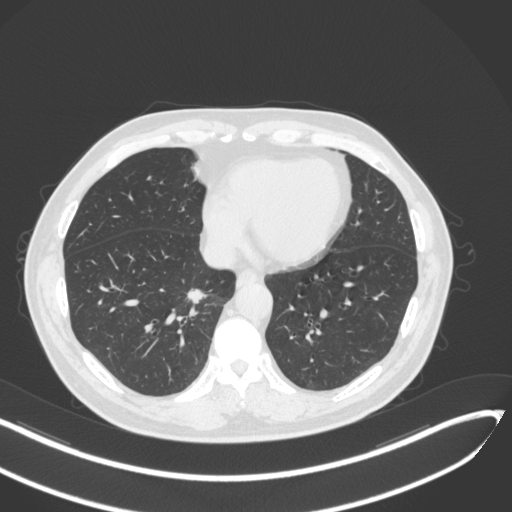
Chest CT, one axial slice. Position 124 of 429 along the scan axis. Reconstruction kernel B31f. 120 kVp. Lung window (W 1500 / L -600 HU). 512 × 512 image matrix, field of view 400 × 400 mm. Patient: male, 62 years. From the clinical record (not read from this slice): clinical TNM (as recorded): T1b N0 M0.
Annotated regions visible in this slice (bounding box drawn by a radiologist):
- lung tumour (recorded histology: adenocarcinoma): bounding box [x1, y1, x2, y2] px = [178, 281, 212, 307]